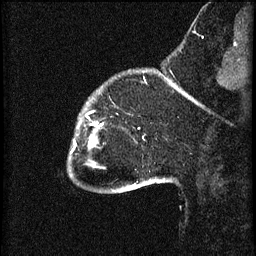
Breast MRI (dynamic contrast-enhanced), one sagittal slice; position 10 of 60 along the scan axis; 3 images stored at this slice position (order not interpretable as contrast timing); 1.5 T; TE 4.2 ms, TR 8.2 ms; 2 mm slice thickness; 256 × 256 image matrix, field of view 180 × 180 mm. Female patient, age 32 years.
Structures marked on this image (semi-automatically segmented with operator editing):
- analysis volume of interest (the breast-tissue region the enhancement analysis was run in; not a lesion): bounding box <69,106,102,165> (left, top, right, bottom; pixels)
- tumour enhancement mask (voxels above the 70 % enhancement threshold inside the analysis volume of interest): <92,126,99,145>